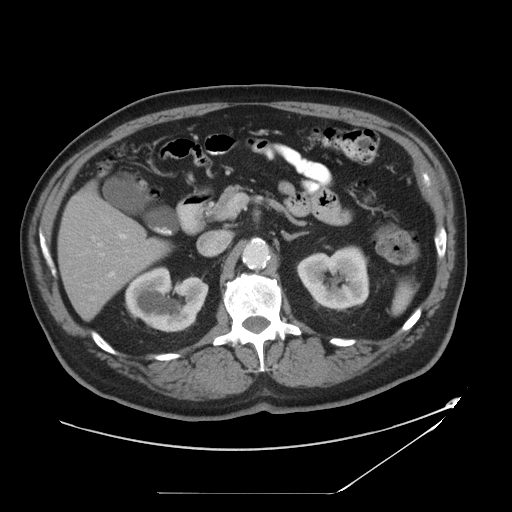
Contrast-enhanced abdominal CT, one axial slice; slice 22 of 49 in the series (ordered by position); reconstruction kernel STANDARD; 120 kVp; intravenous contrast given; soft-tissue window (W 400 / L 40 HU); 5 mm slice thickness; 512 × 512 image matrix, field of view 461 × 461 mm. Male patient, age 72 years. Case-level facts recorded for this patient, not image findings: diagnosis: colorectal cancer liver metastases, imaged before liver resection; multiple liver metastases: no; largest metastasis: 2.5 cm.
Annotated regions visible in this slice (manually delineated by an expert):
- hepatic veins: bounding box <92,221,110,247> (left, top, right, bottom; pixels)
- liver: <60,187,166,318>
- planned liver remnant (the part of the liver to remain after resection): <60,187,166,319>
- portal vein (with intrahepatic branches): <108,233,127,277>